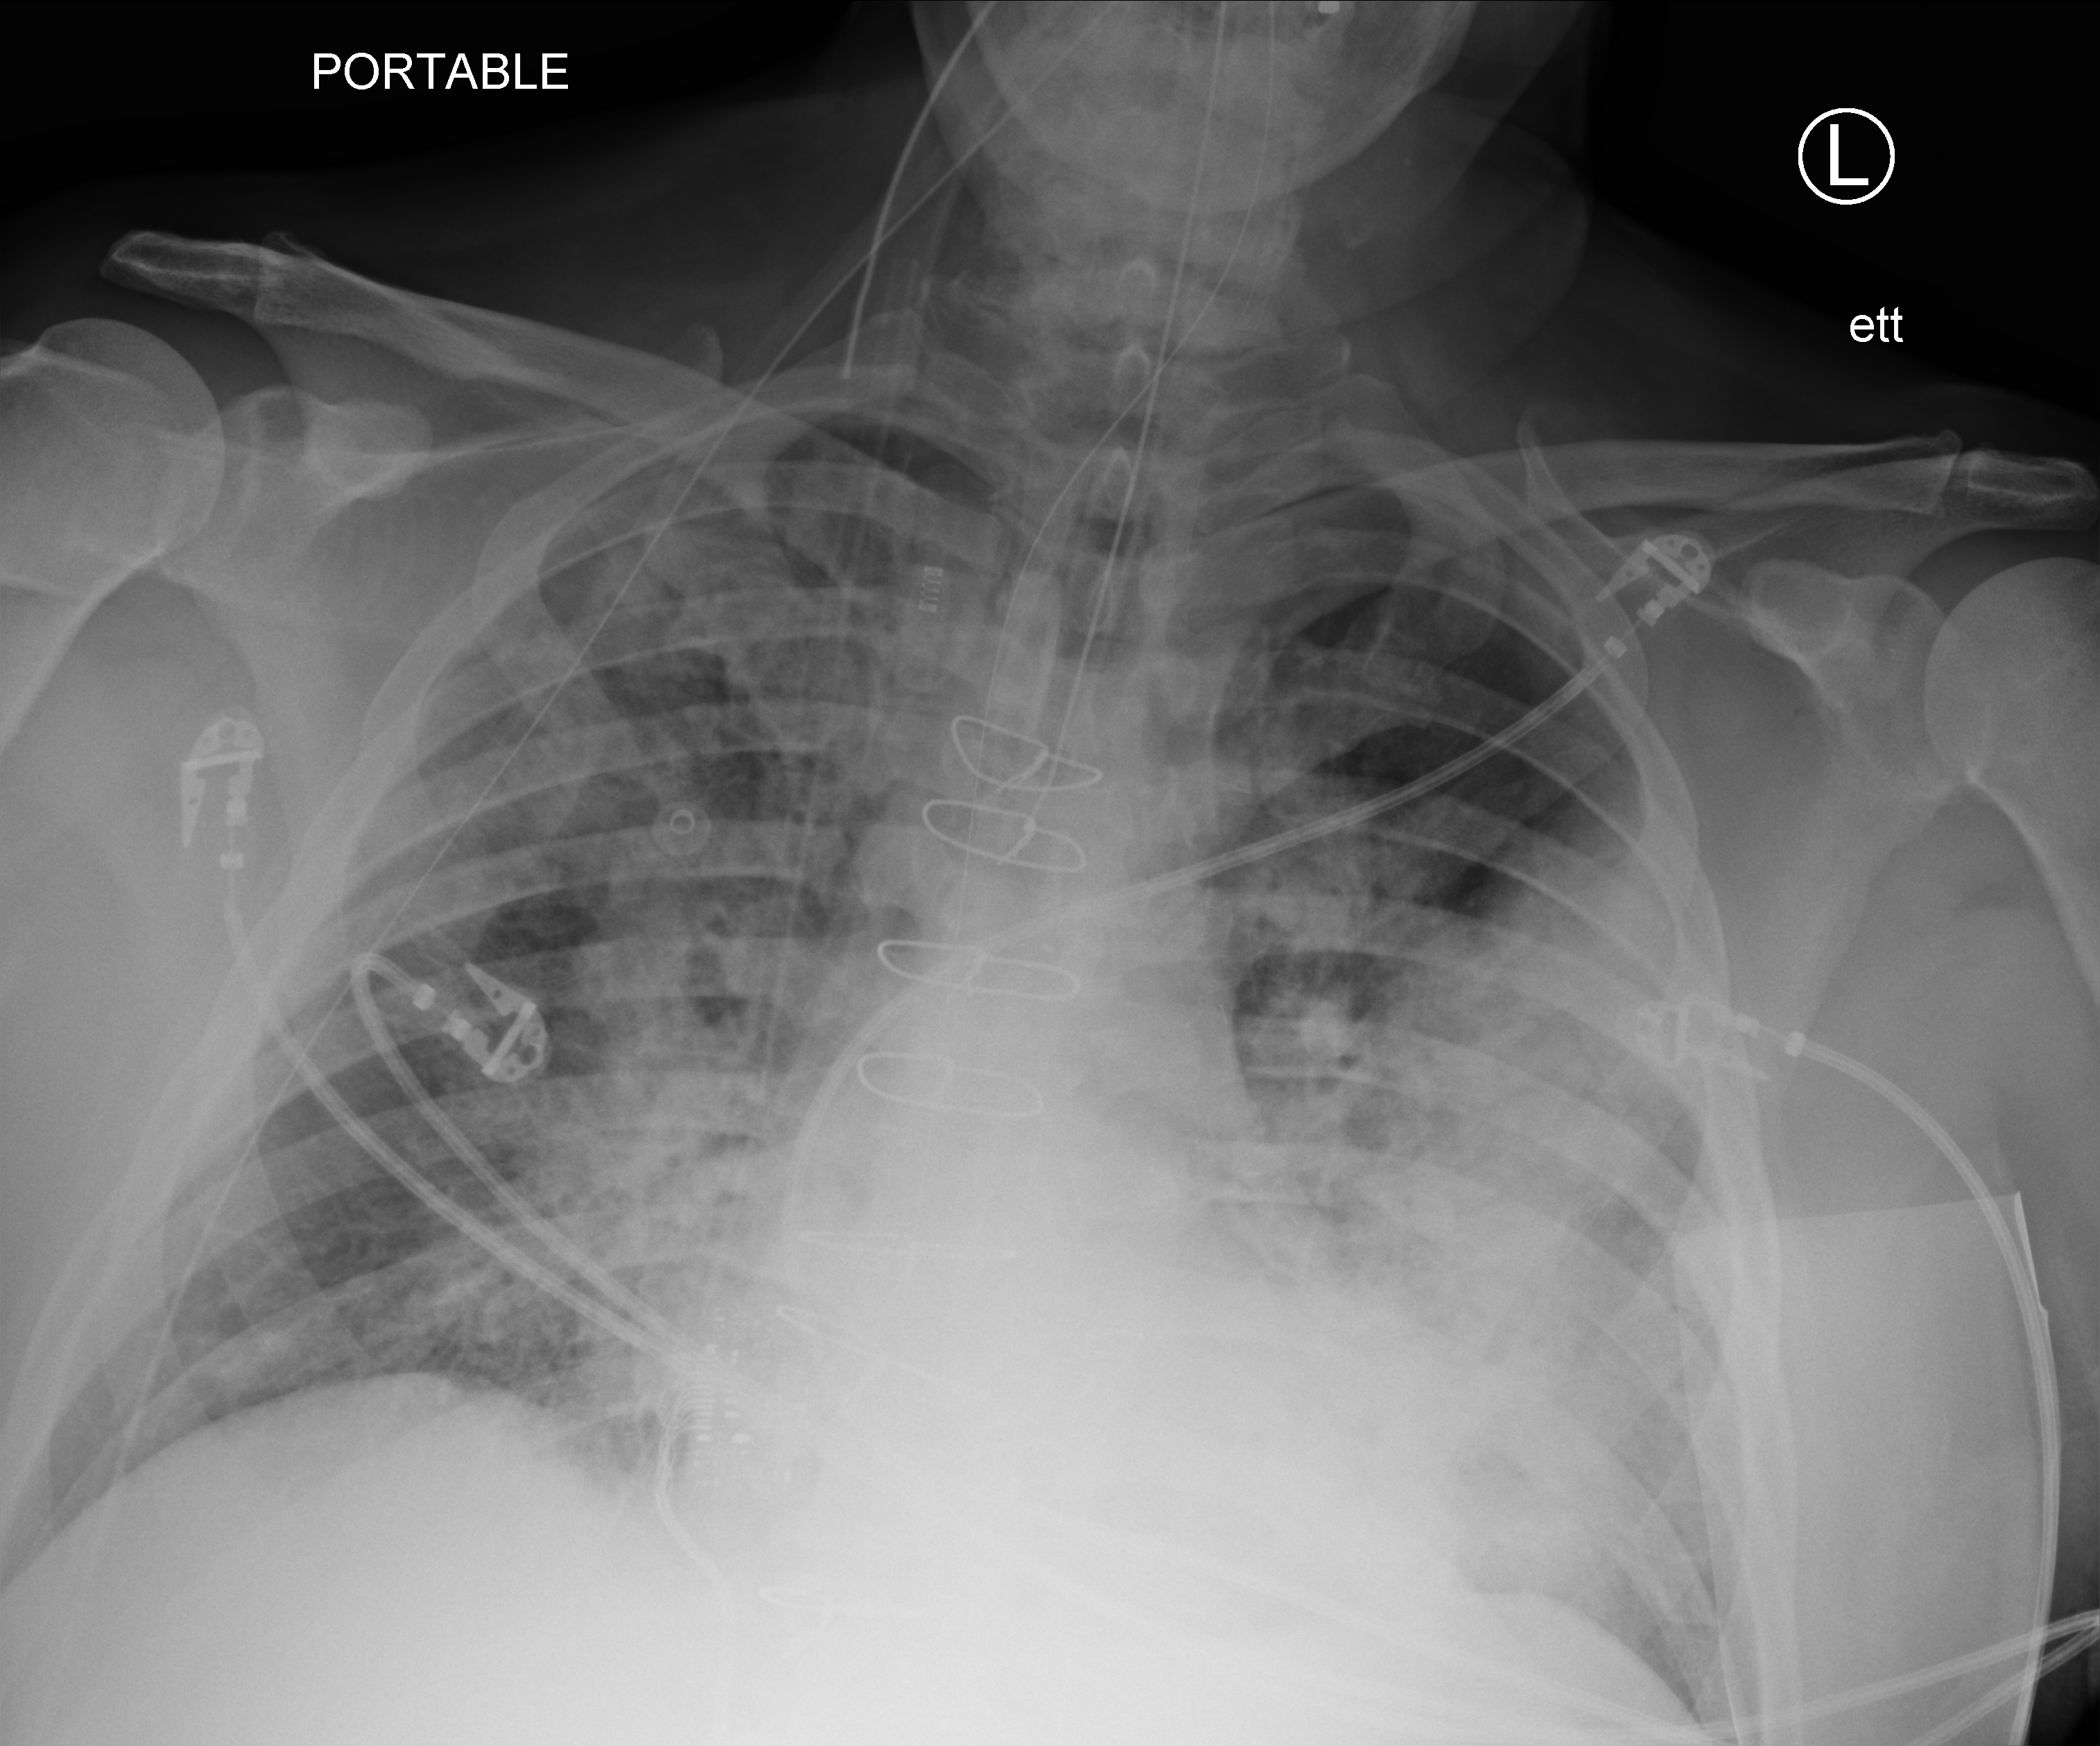
Portable chest radiograph, anteroposterior (AP) projection. Patient hospitalised with COVID-19; male, aged 60–74 years.
Hospital-stay facts (about this admission, not read from this image; timing relative to this image not recorded): other chronic lung disease (admission record): no; length of hospital stay: 44 days.